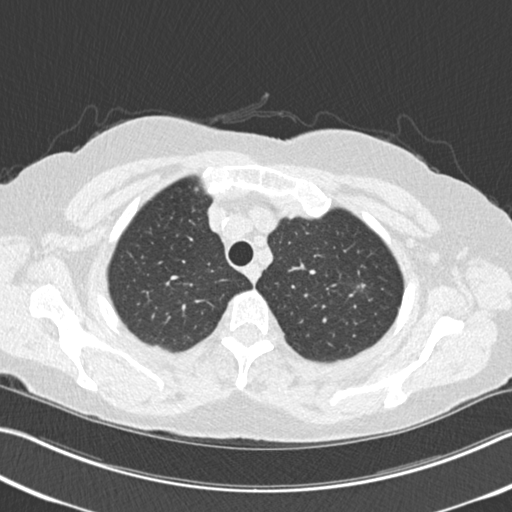
Low-dose screening chest CT, axial slice, second screening round (one year after baseline), lung window (W 1500 / L -600 HU). Female, age 64 years at enrolment. Former smoker at enrolment.
Lesion marked by an expert reader, bounding box <346,269,381,303> (left, top, right, bottom; pixels). The exam's reader record, not a measurement of the box and not confirmed to be the same lesion: non-calcified nodule or mass ≥4 mm, left upper lobe, 13 × 10 mm, spiculated (stellate) margins, soft tissue attenuation, pre-existing on the prior screen: yes; interval growth: yes. Lung cancer was diagnosed 106 days after this screen: signet ring cell carcinoma, right upper lobe, poorly differentiated (G3), stage IA (AJCC 6th edition), 15 mm at pathology.